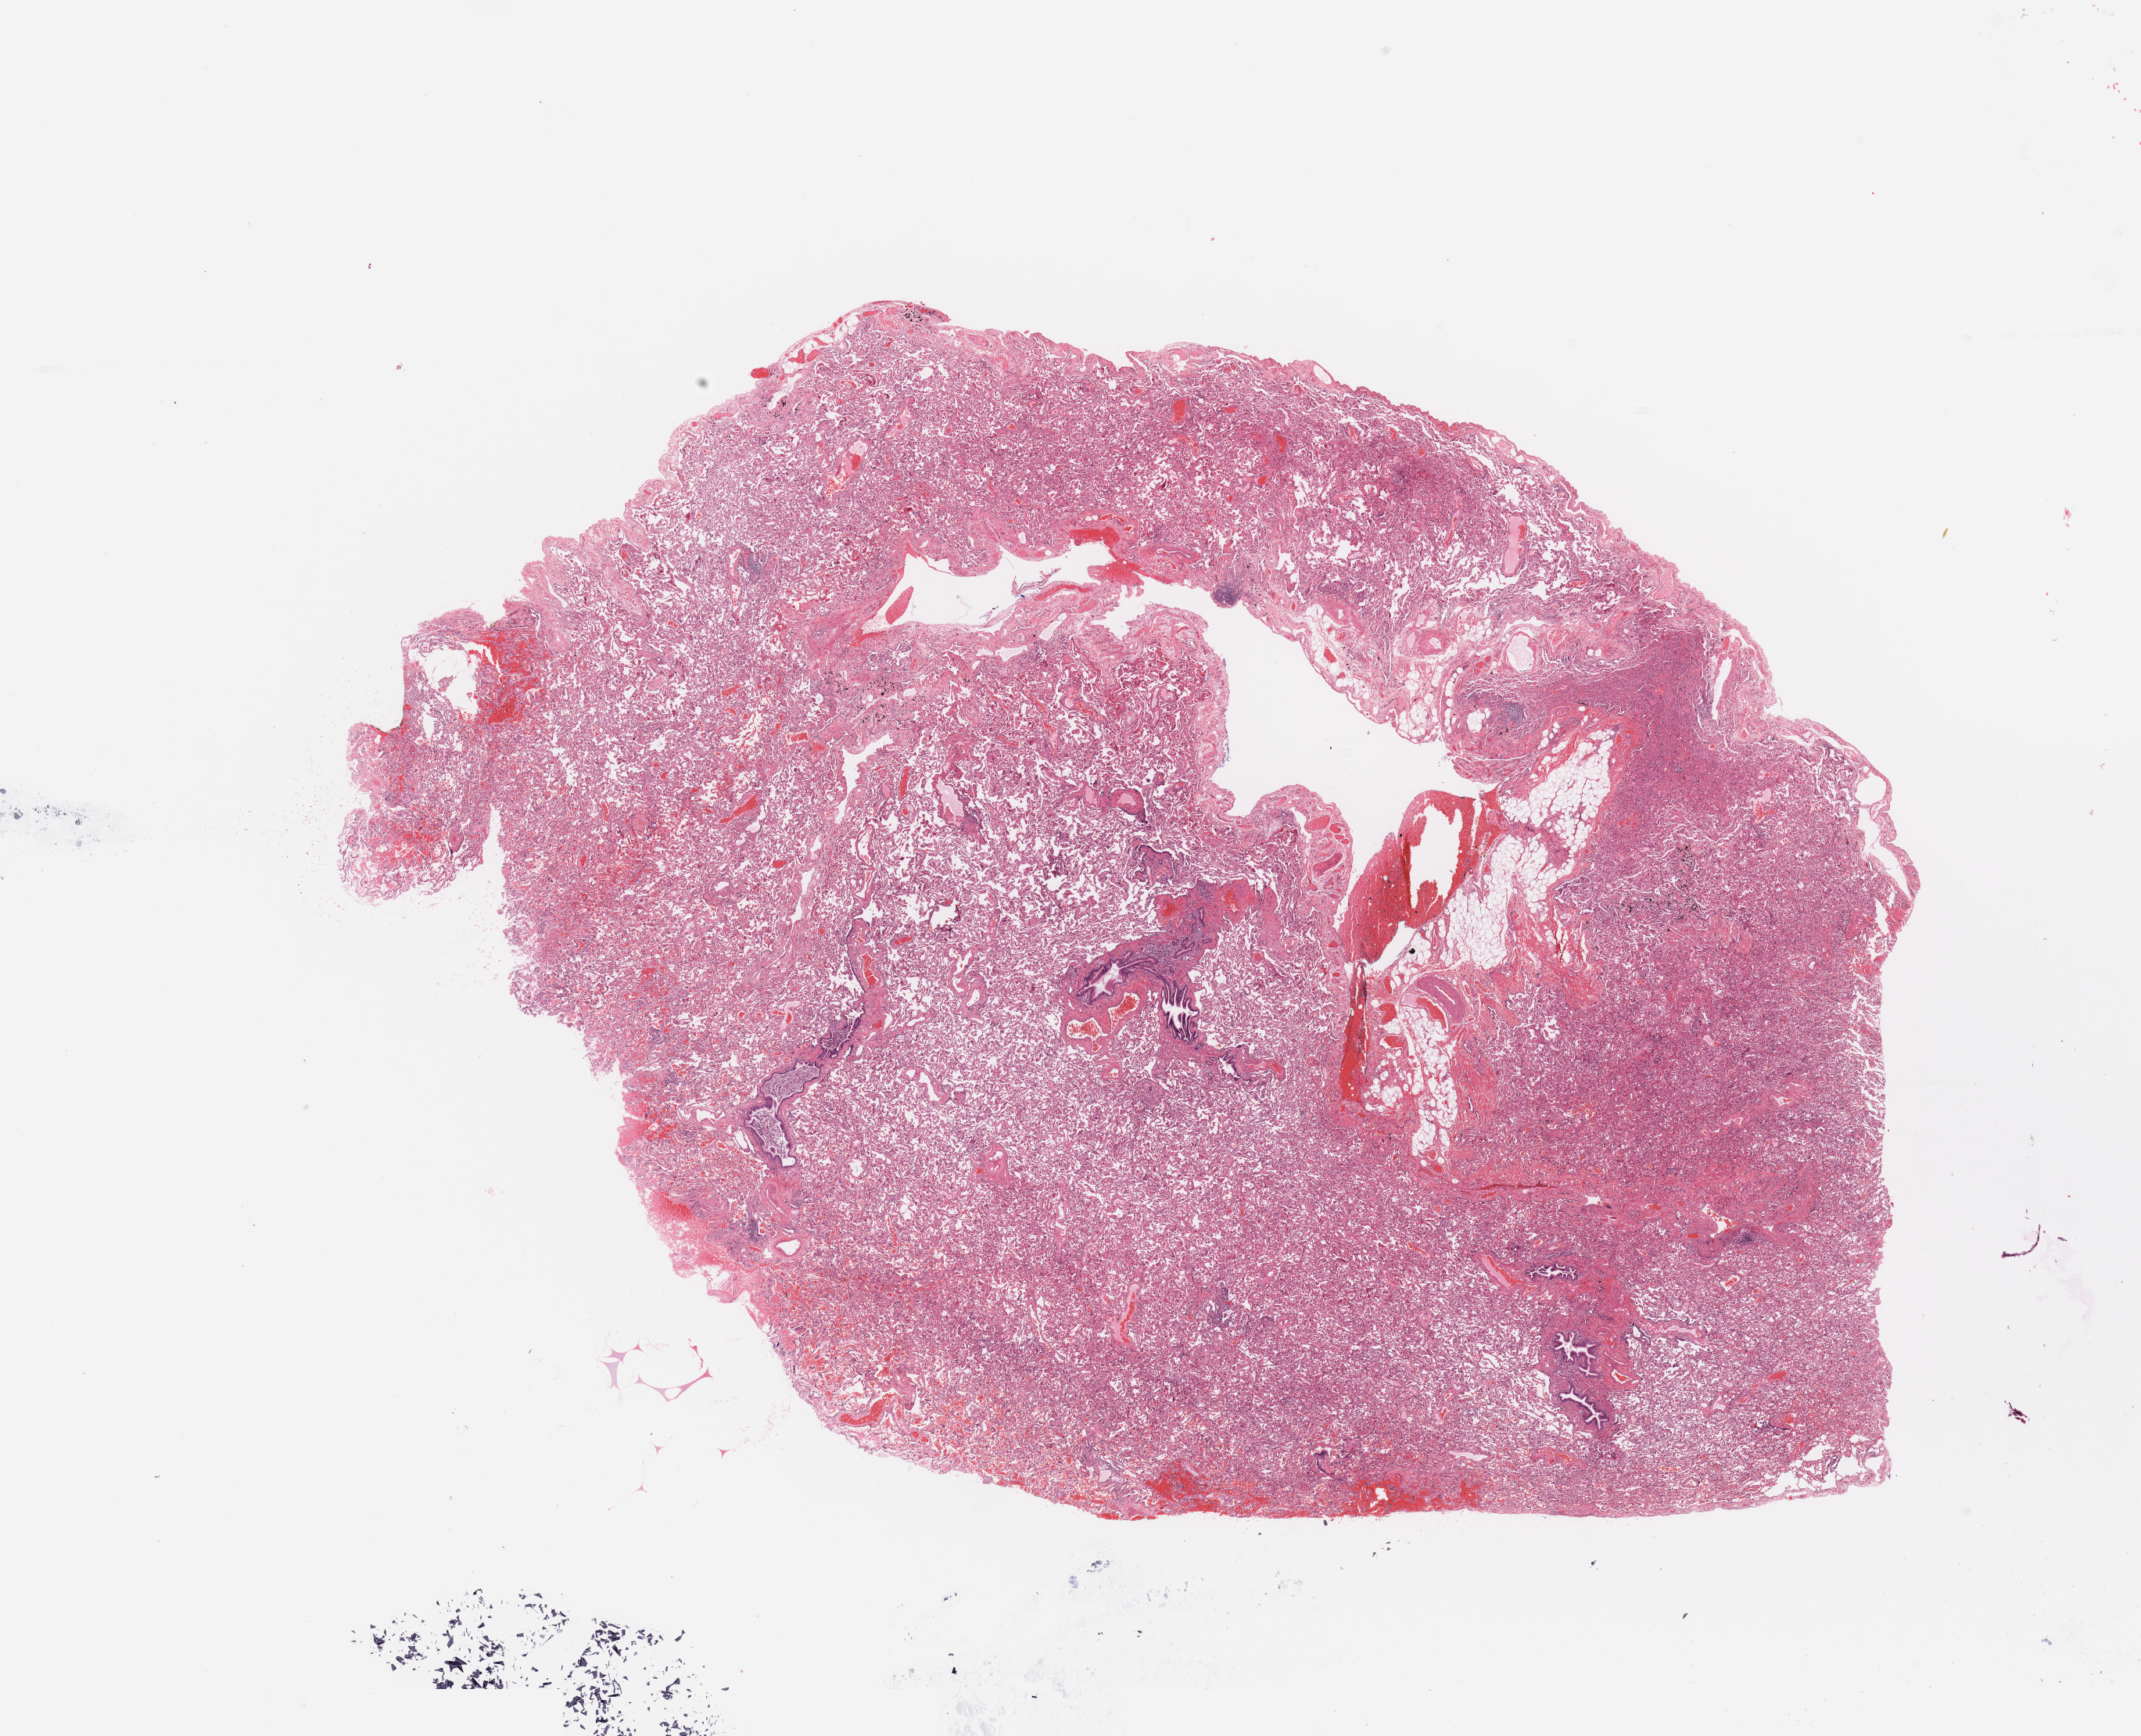
H&E whole-slide image — low-resolution overview of the scanned area, about 21.7 x 17.6 mm (from a 20x scan). Normal (non-tumour) tissue sample, sampled site: lung. Patient: male, age 58 years.
- this section: normal (non-tumour) tissue from the same patient
- patient diagnosis: Adenocarcinoma, NOS